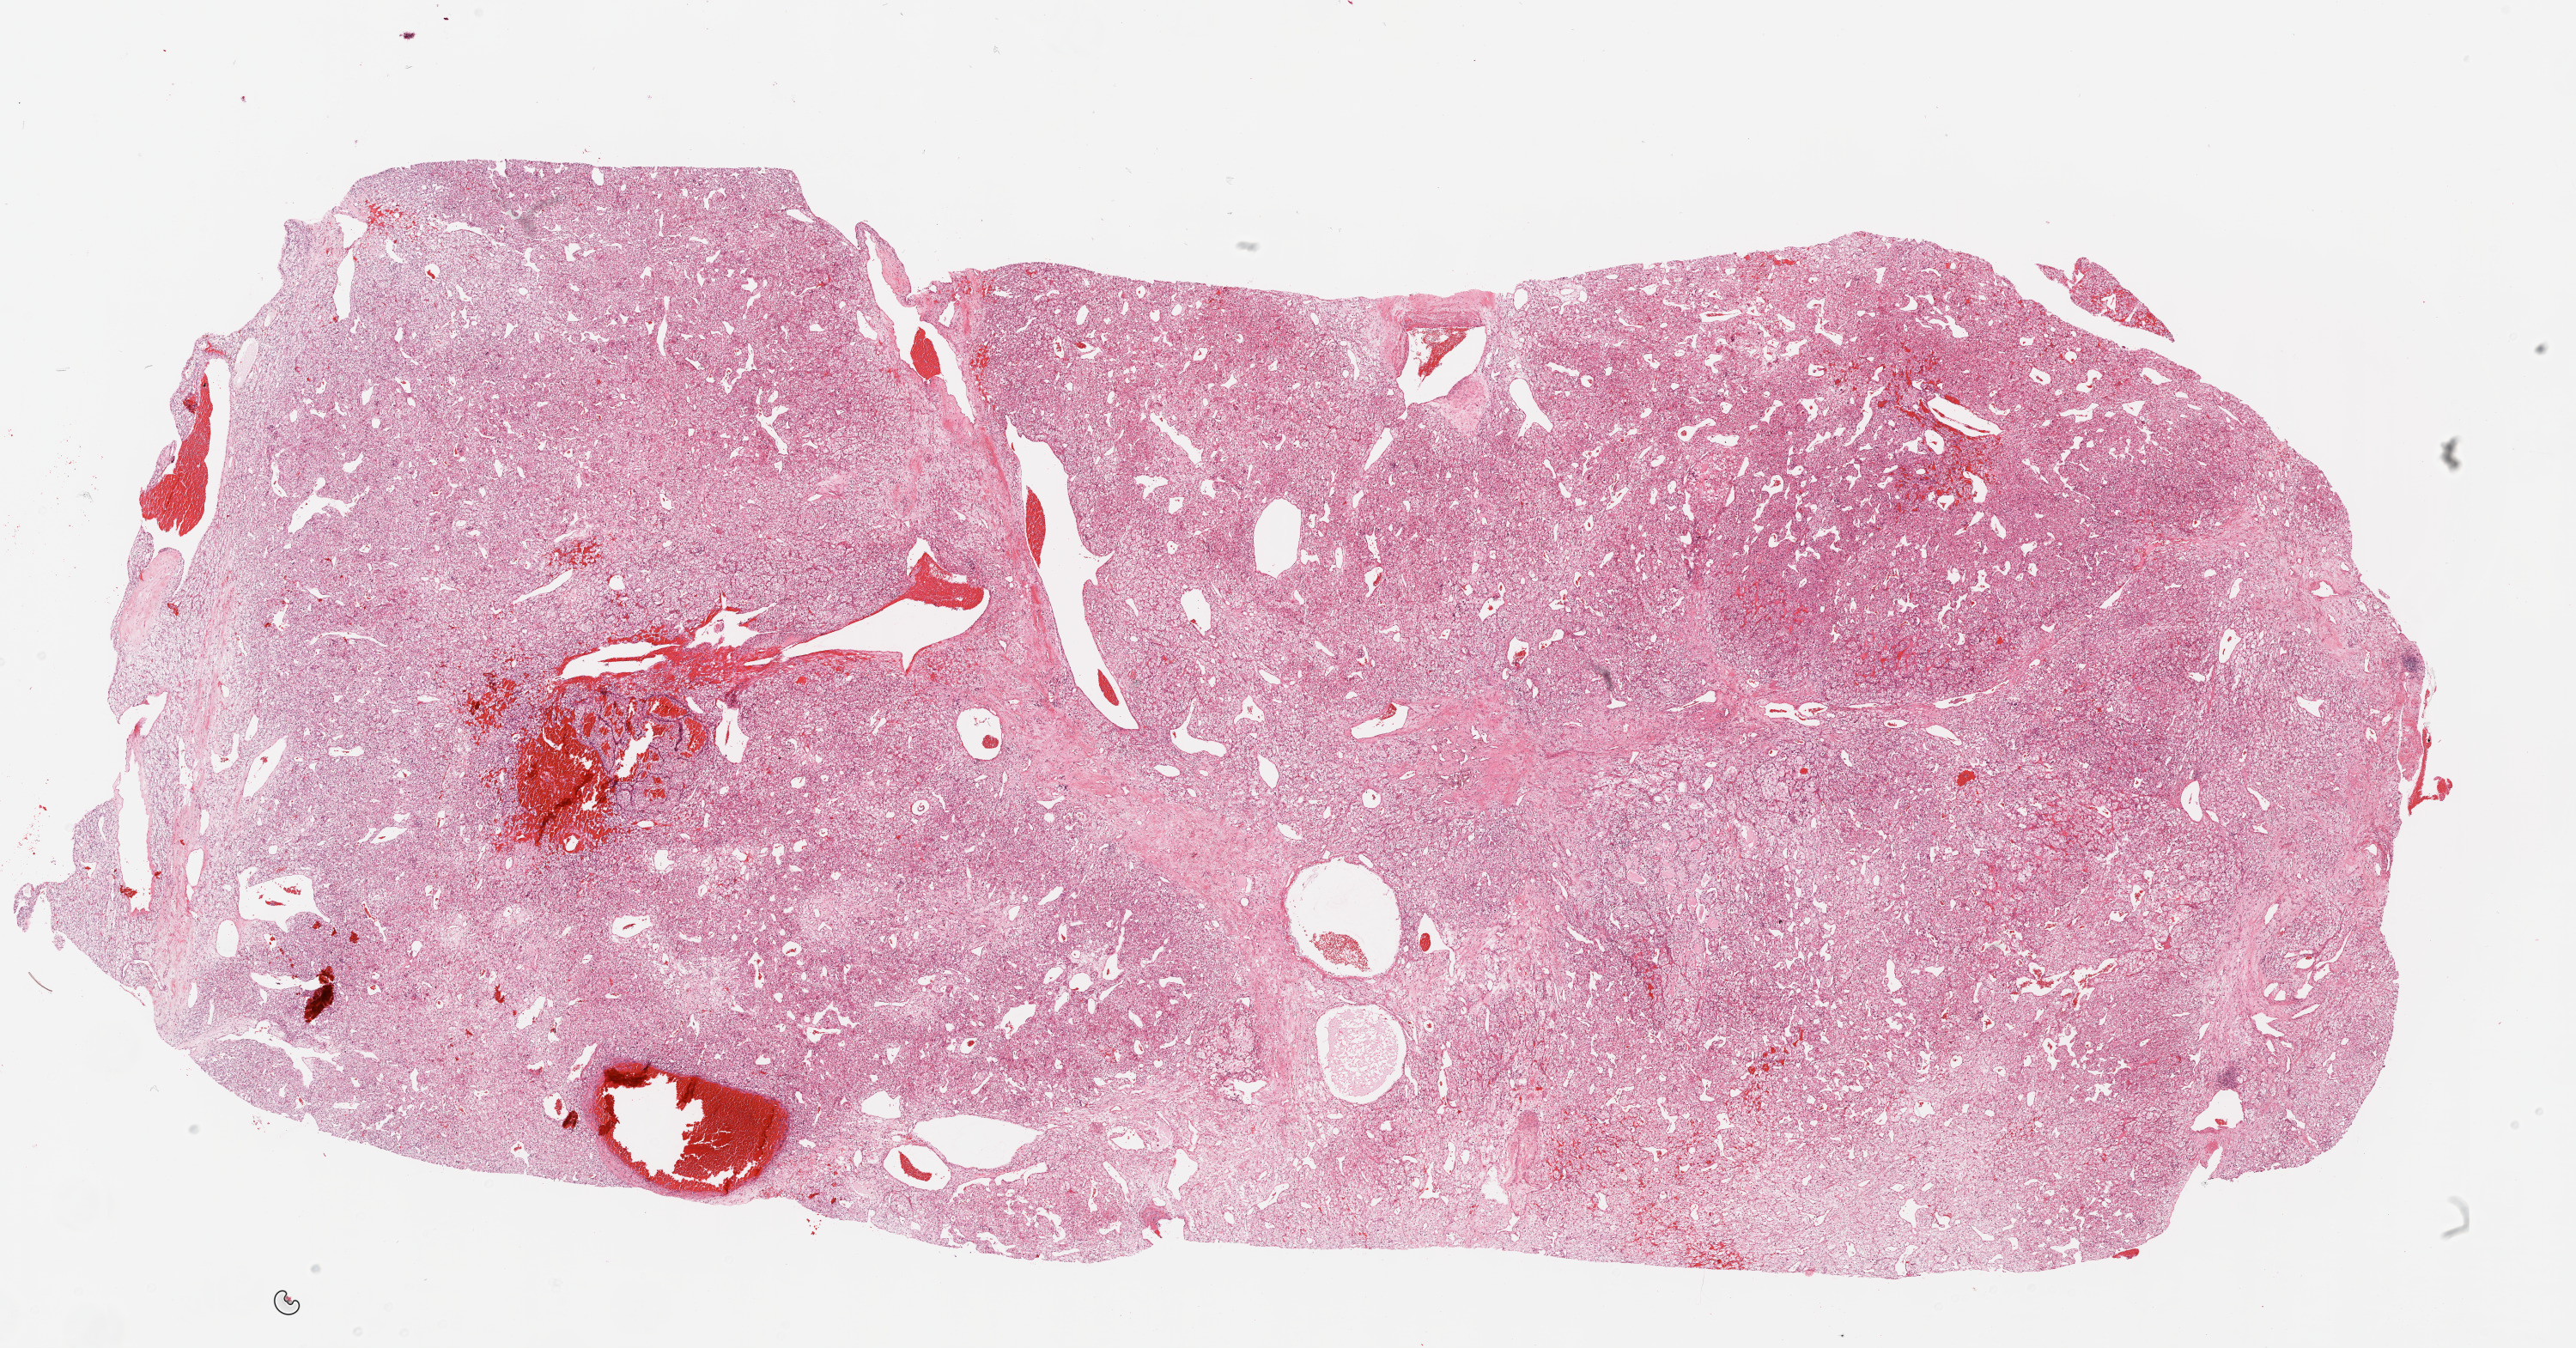
Whole-slide histology image, H&E-stained — low-resolution overview of the scanned area, about 24.1 x 12.6 mm (acquisition: 20x scan); FFPE section; sample: primary tumour, kidney. Patient: female, age at initial diagnosis 62 years. Histologic grade: G2 (moderately differentiated).
TNM: T1b N0 M0. AJCC pathologic stage: I. Laterality: left. Pathologic diagnosis: Clear cell adenocarcinoma, NOS.